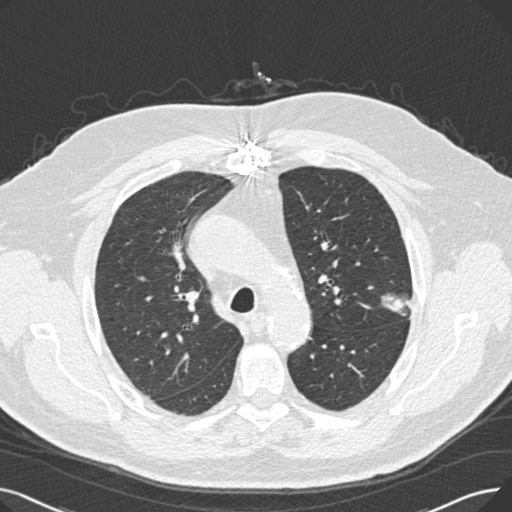
Low-dose screening chest CT, one axial slice; slice 185 of 269 in the series (ordered by position); lung window (W 1500 / L -600 HU); 1 mm slice thickness; 512 × 512 image matrix, field of view 370 × 370 mm.
Annotated regions visible in this slice (expert manual segmentation):
- lesion 1 (tumor, upper lobe of left lung): bounding box [x1, y1, x2, y2] px = [381, 294, 410, 316]